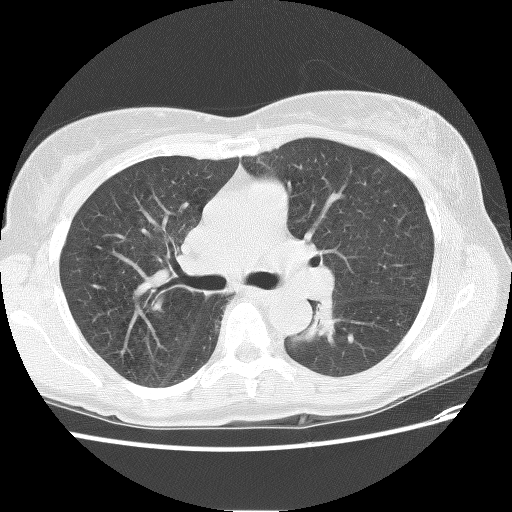
Low-dose screening chest CT, axial slice, first (baseline) screen, lung window (W 1500 / L -600 HU), 2.5 mm slice thickness, lung (sharp) reconstruction kernel (BONE), slice 44 of 118 in the series. Female participant, aged 62 years at enrolment. Former smoker at enrolment.
Expert-annotated lung lesion, bounding box <289,300,344,343> (left, top, right, bottom; pixels). Screening reader's record for this exam: no non-calcified nodule ≥4 mm recorded. Lung cancer was diagnosed 898 days after this screen: squamous cell carcinoma, NOS, left lower lobe, stage IIIB (AJCC 6th edition), 31 mm at pathology.